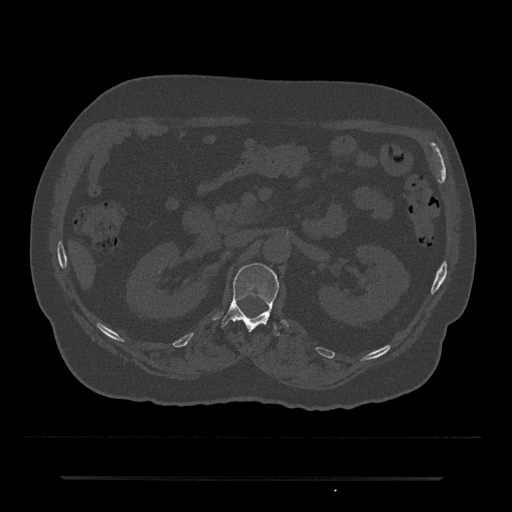
CT including the spine, one axial slice. Bone window (W 1800 / L 400 HU). 0.5 mm slice thickness. 512 × 512 image matrix. Patient: male, 69 years. Case-level facts recorded for this patient, not image findings: primary cancer: prostate.
Annotated regions visible in this slice (semi-automatic segmentation, software-assisted and operator-edited):
- L1 vertebra: box from (x=221, y=263) to (x=279, y=336) px